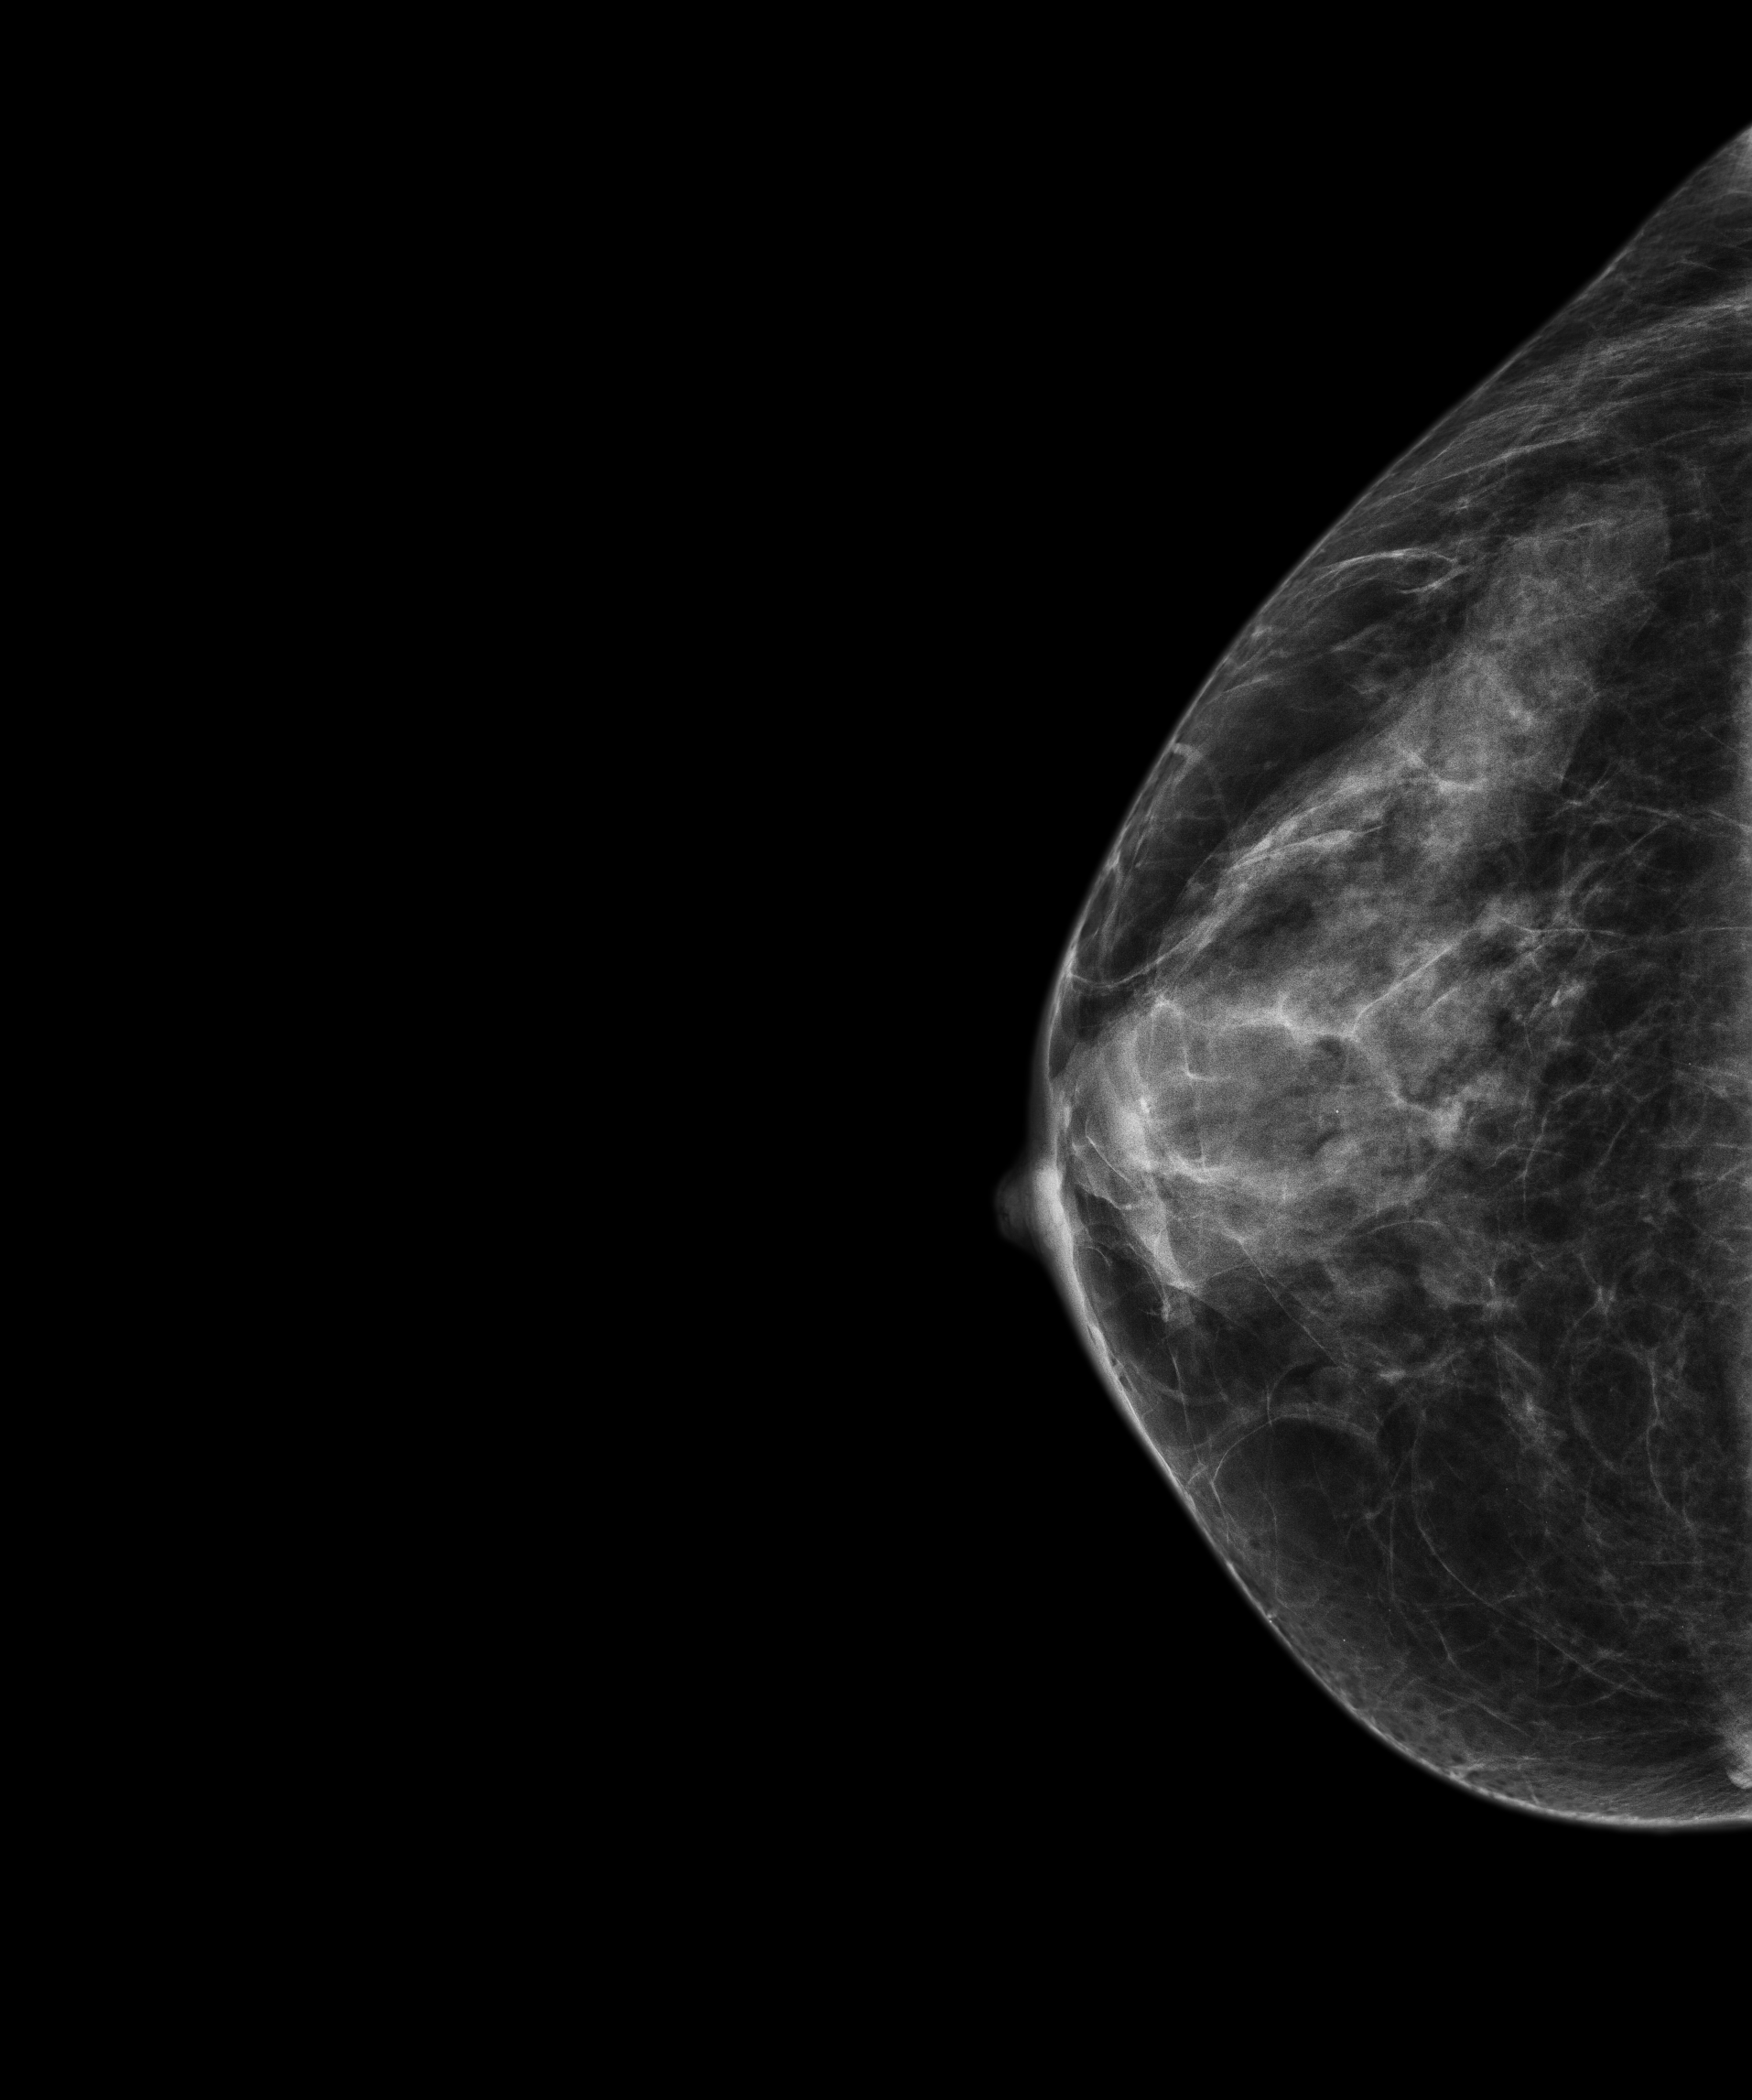
Digital mammogram (FFDM); right breast; craniocaudal (CC) view; screening examination; compressed breast thickness 34.2 mm; system: Senographe Pristina. Female patient, age 48 years.
Breast density at the screening exam (both breasts): heterogeneously dense (BI-RADS density category c). Final BI-RADS assessment for this screening round (tomosynthesis exam, both breasts): category 2. Recall: no recall after this screen.